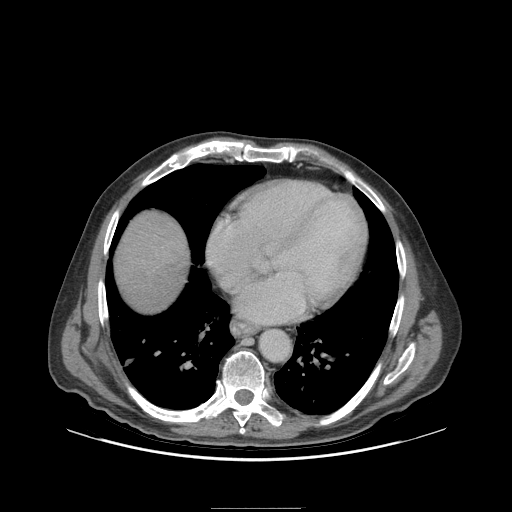
Contrast-enhanced abdominal CT (liver protocol), one axial slice. Slice 96 of 105 in the series (ordered by position). Reconstruction kernel STANDARD. 140 kVp. Soft-tissue window (W 400 / L 40 HU). 512 × 512 image matrix. From the clinical record (not read from this slice): diagnosis: hepatocellular carcinoma (patient treated with transarterial chemoembolisation; whether this scan precedes or follows treatment is not stated here); TNM stage (as recorded): Stage-I; Child-Pugh class: A; tumour nodularity: uninodular; tumour size: 5.1 cm.
Annotated regions visible in this slice (semi-automatically segmented with operator editing):
- liver parenchyma outside the tumour (the mass and vessels are separate outlines, so this box may not span the whole liver): box from (x=114, y=210) to (x=188, y=310) px